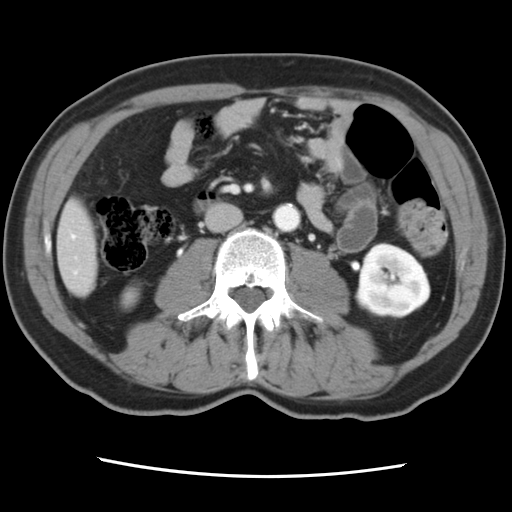
Contrast-enhanced abdominal CT, one axial slice. Position 18 of 83 along the scan axis. 120 kVp. Soft-tissue window (W 400 / L 40 HU). 512 × 512 image matrix. Male patient, age 69 years. From the clinical record (not read from this slice): diagnosis: colorectal cancer liver metastases, imaged before liver resection; multiple liver metastases: yes; largest metastasis: 3.5 cm; disease in both lobes: no.
Outlined on this slice (manually delineated by an expert):
- hepatic veins: bounding box [x1, y1, x2, y2] px = [72, 235, 77, 273]
- liver: [59, 202, 98, 295]
- planned liver remnant (the part of the liver to remain after resection): [59, 202, 98, 295]